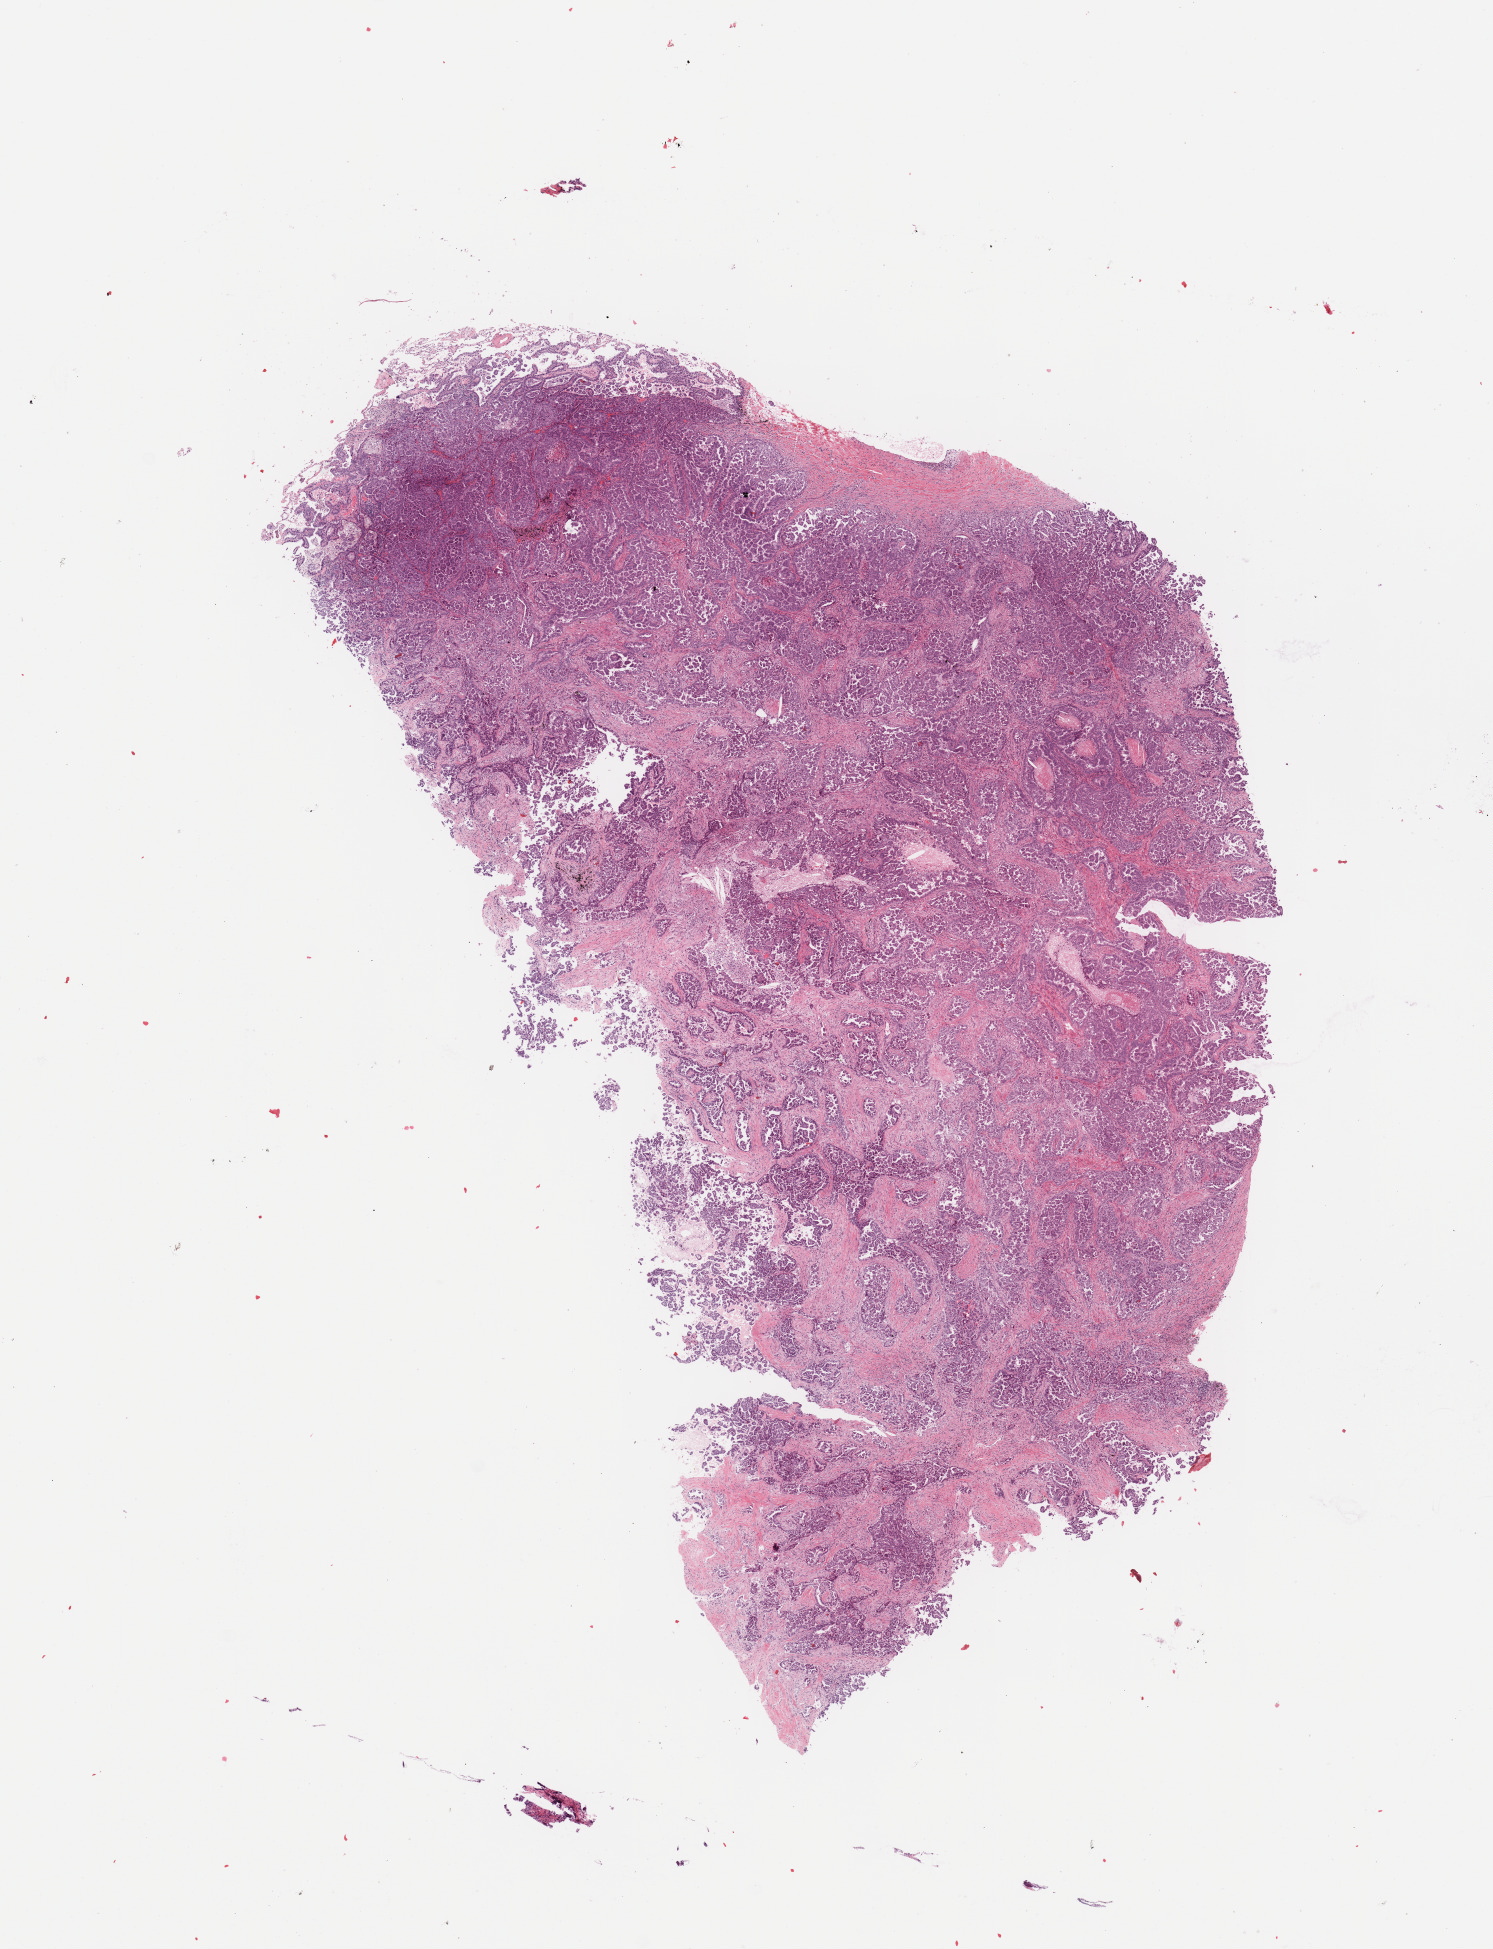
H&E whole-slide image, low-resolution overview of the scanned area, about 11.8 x 15.4 mm. Lung, tumour tissue. 68-year-old male patient. Histologic grade: G3 (poorly differentiated).
Diagnosis: Adenocarcinoma, NOS. AJCC pathologic stage: IIIA.